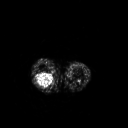
FDG PET of an extremity soft-tissue mass (from a PET/CT study), one axial slice; slice 180 of 267 in the series (ordered by position); 3.27 mm slice thickness; 128 × 128 image matrix, field of view 500 × 500 mm. Female patient, age 62 years. From the clinical record (not read from this slice): histological type: liposarcoma; site of the primary tumour: right thigh.
Outlined on this slice (expert contour drawn on MRI and transferred to this co-registered scan by the dataset authors):
- gross tumour volume (mass): box from (x=35, y=72) to (x=55, y=88) px